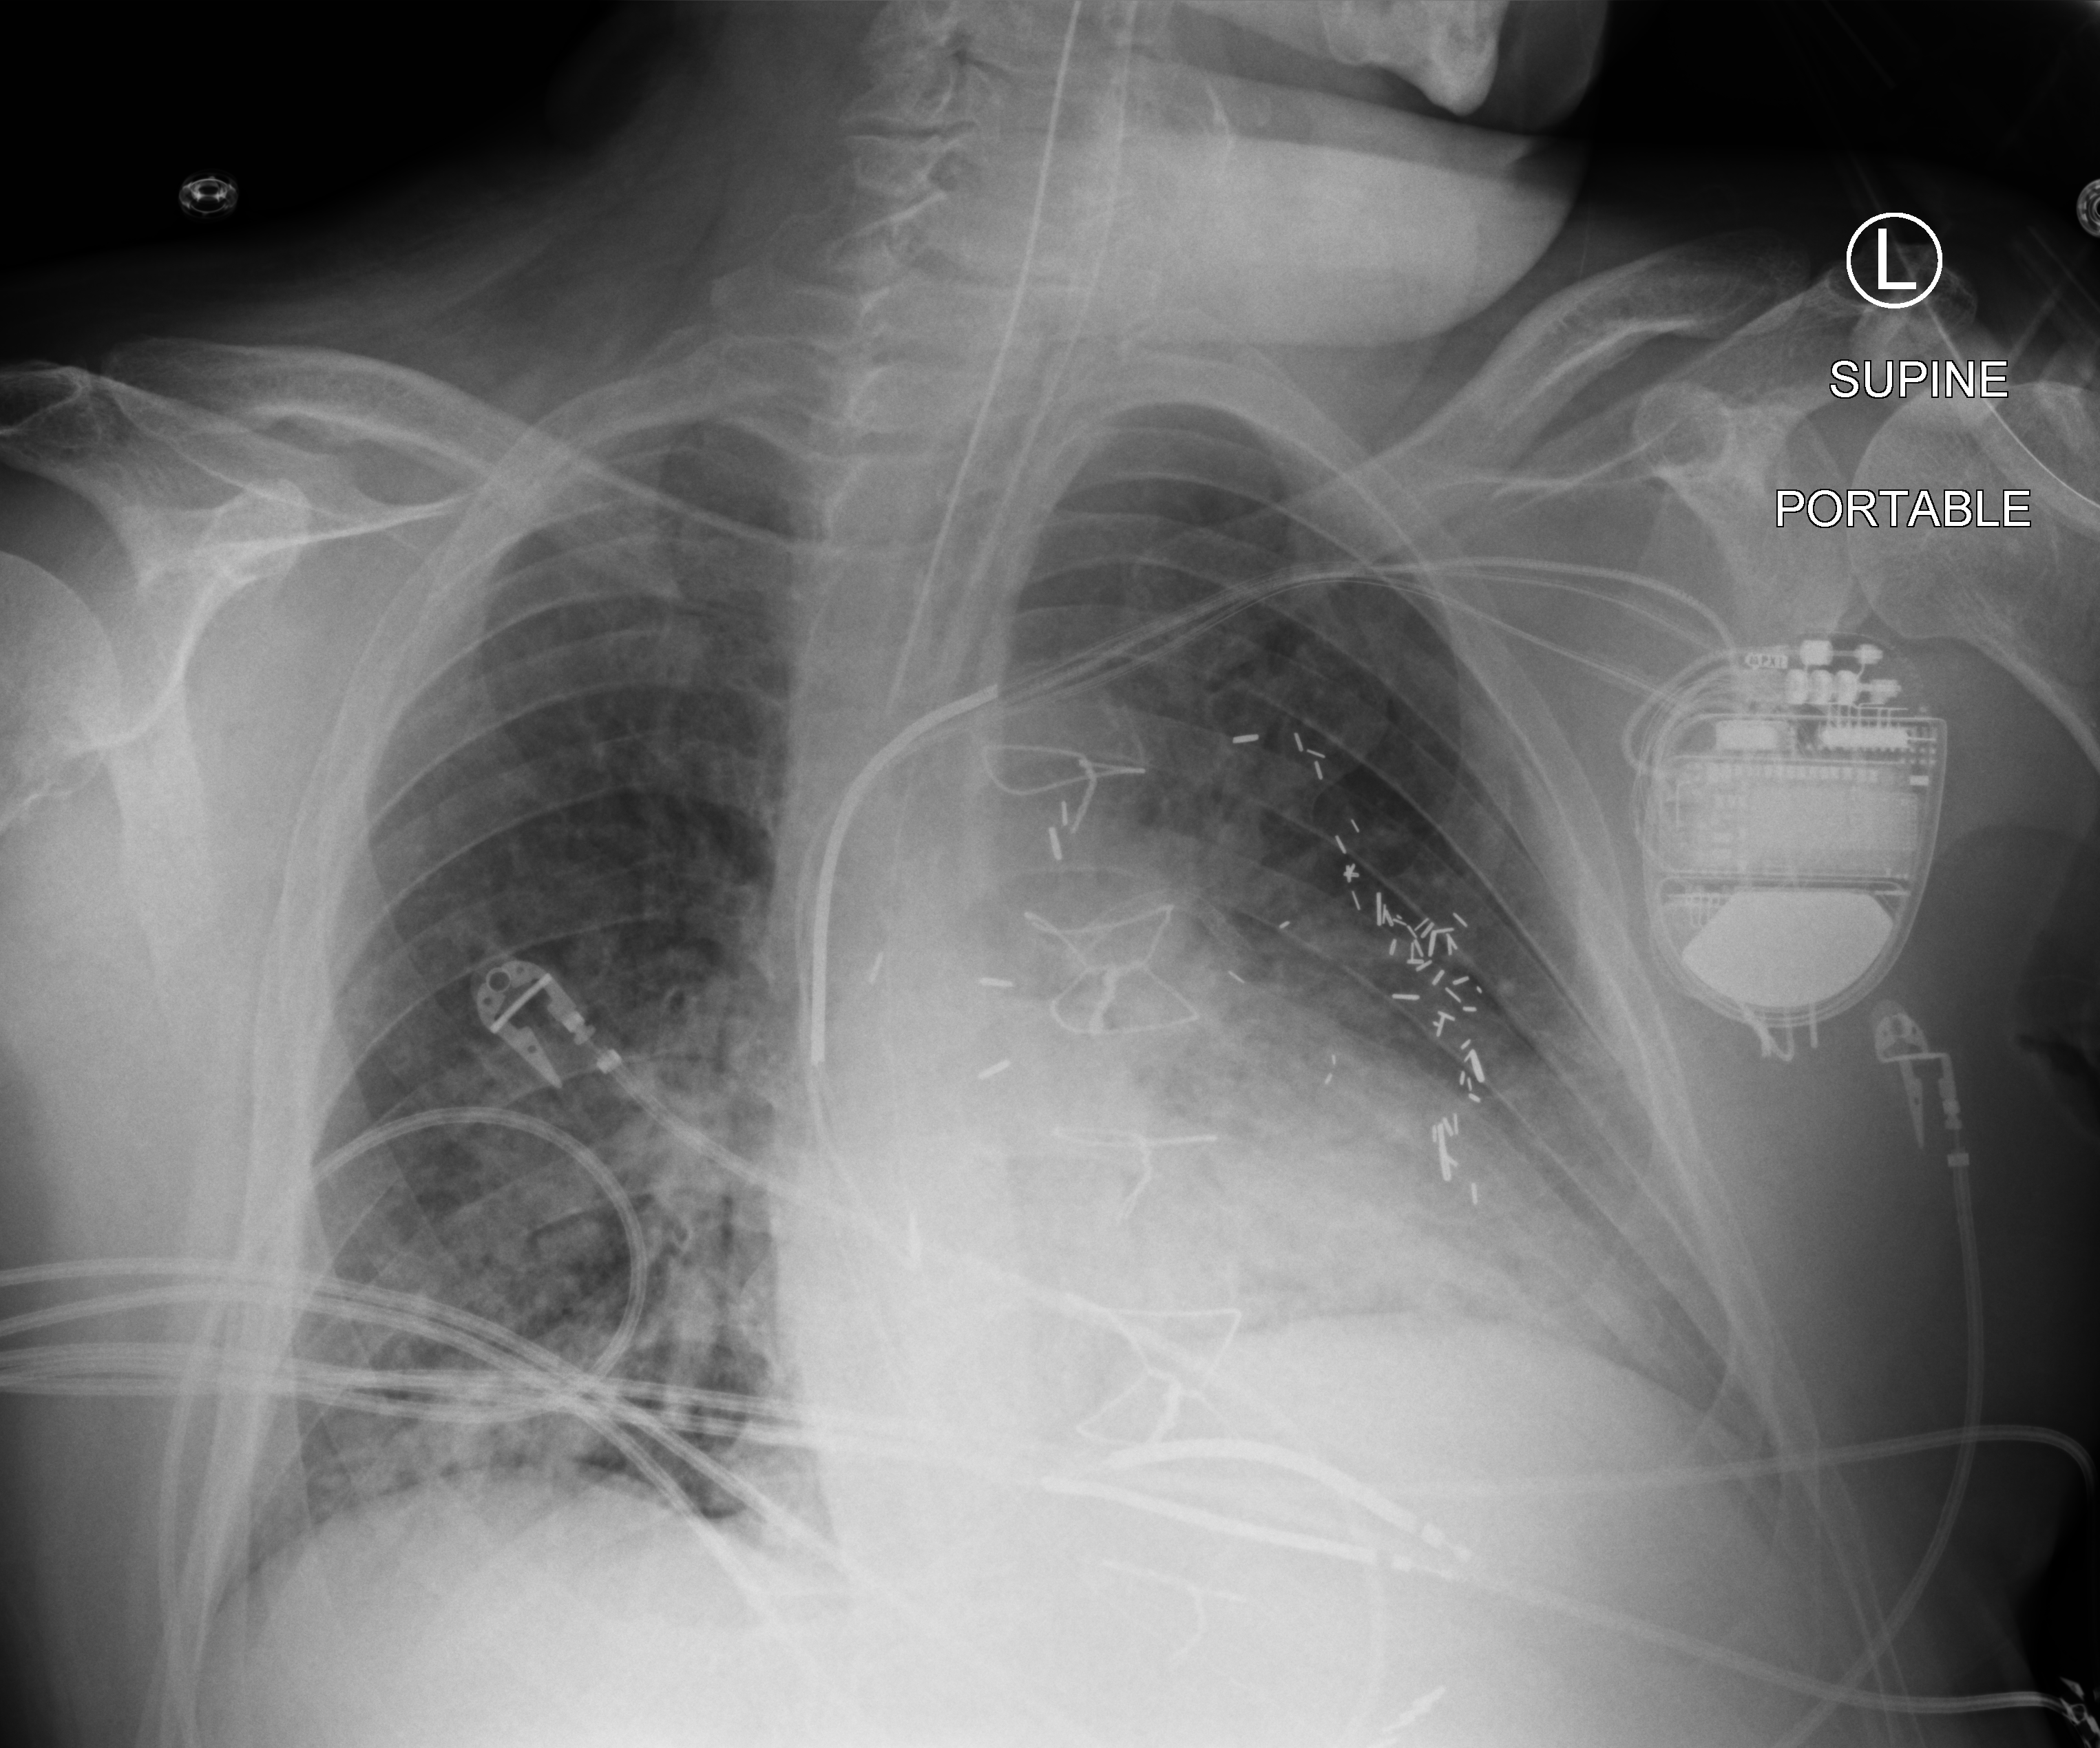
Portable chest radiograph. Male patient hospitalised with COVID-19, age 60–74 years.
From the hospital-stay record, not from the radiograph (when in the stay this image was taken is not recorded): smoking status (admission record): never.